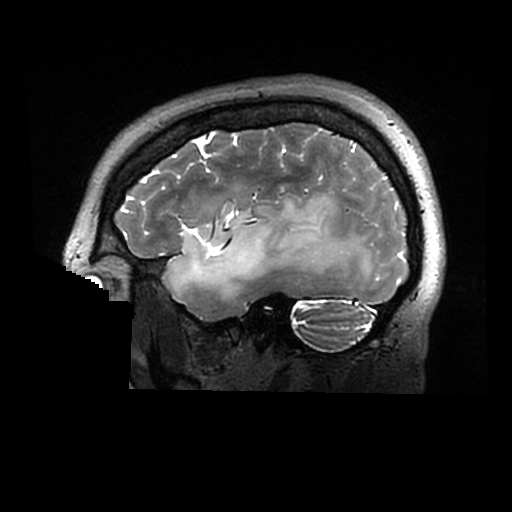
Brain MRI from a brain-tumour surgery series, one sagittal slice; slice 226 of 320 in the series (ordered by position); 0.6 mm slice thickness; 512 × 512 image matrix, field of view 240 × 240 mm. From the clinical record (not read from this slice): histopathology: Astrocytoma; WHO grade: 2; IDH mutation: yes.
Outlined on this slice (manually delineated by an expert):
- tumour: bounding box <167,194,378,300> (left, top, right, bottom; pixels)